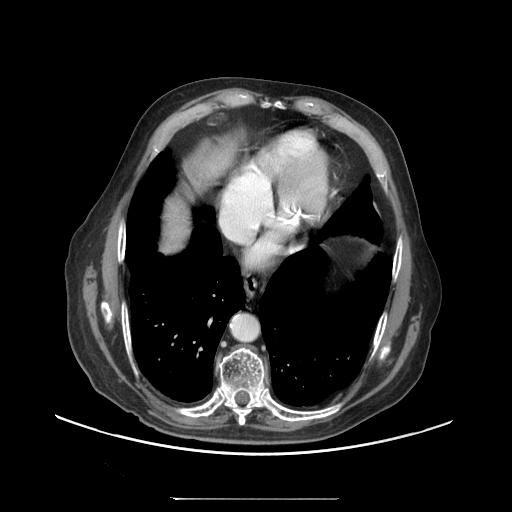
Contrast-enhanced abdominal CT (liver protocol), one axial slice. Slice 88 of 97 in the series (ordered by position). Reconstruction kernel STANDARD. Soft-tissue window (W 400 / L 40 HU). 2.5 mm slice thickness. 512 × 512 image matrix, field of view 450 × 450 mm. Case-level facts recorded for this patient, not image findings: diagnosis: hepatocellular carcinoma (patient treated with transarterial chemoembolisation; whether this scan precedes or follows treatment is not stated here); TNM stage (as recorded): Stage-IIIC; Child-Pugh class: A; tumour differentiation: well differentiated; tumour nodularity: uninodular.
Structures marked on this image (semi-automatic segmentation, software-assisted and operator-edited):
- liver parenchyma outside the tumour (the mass and vessels are separate outlines, so this box may not span the whole liver): bounding box <164,200,188,252> (left, top, right, bottom; pixels)